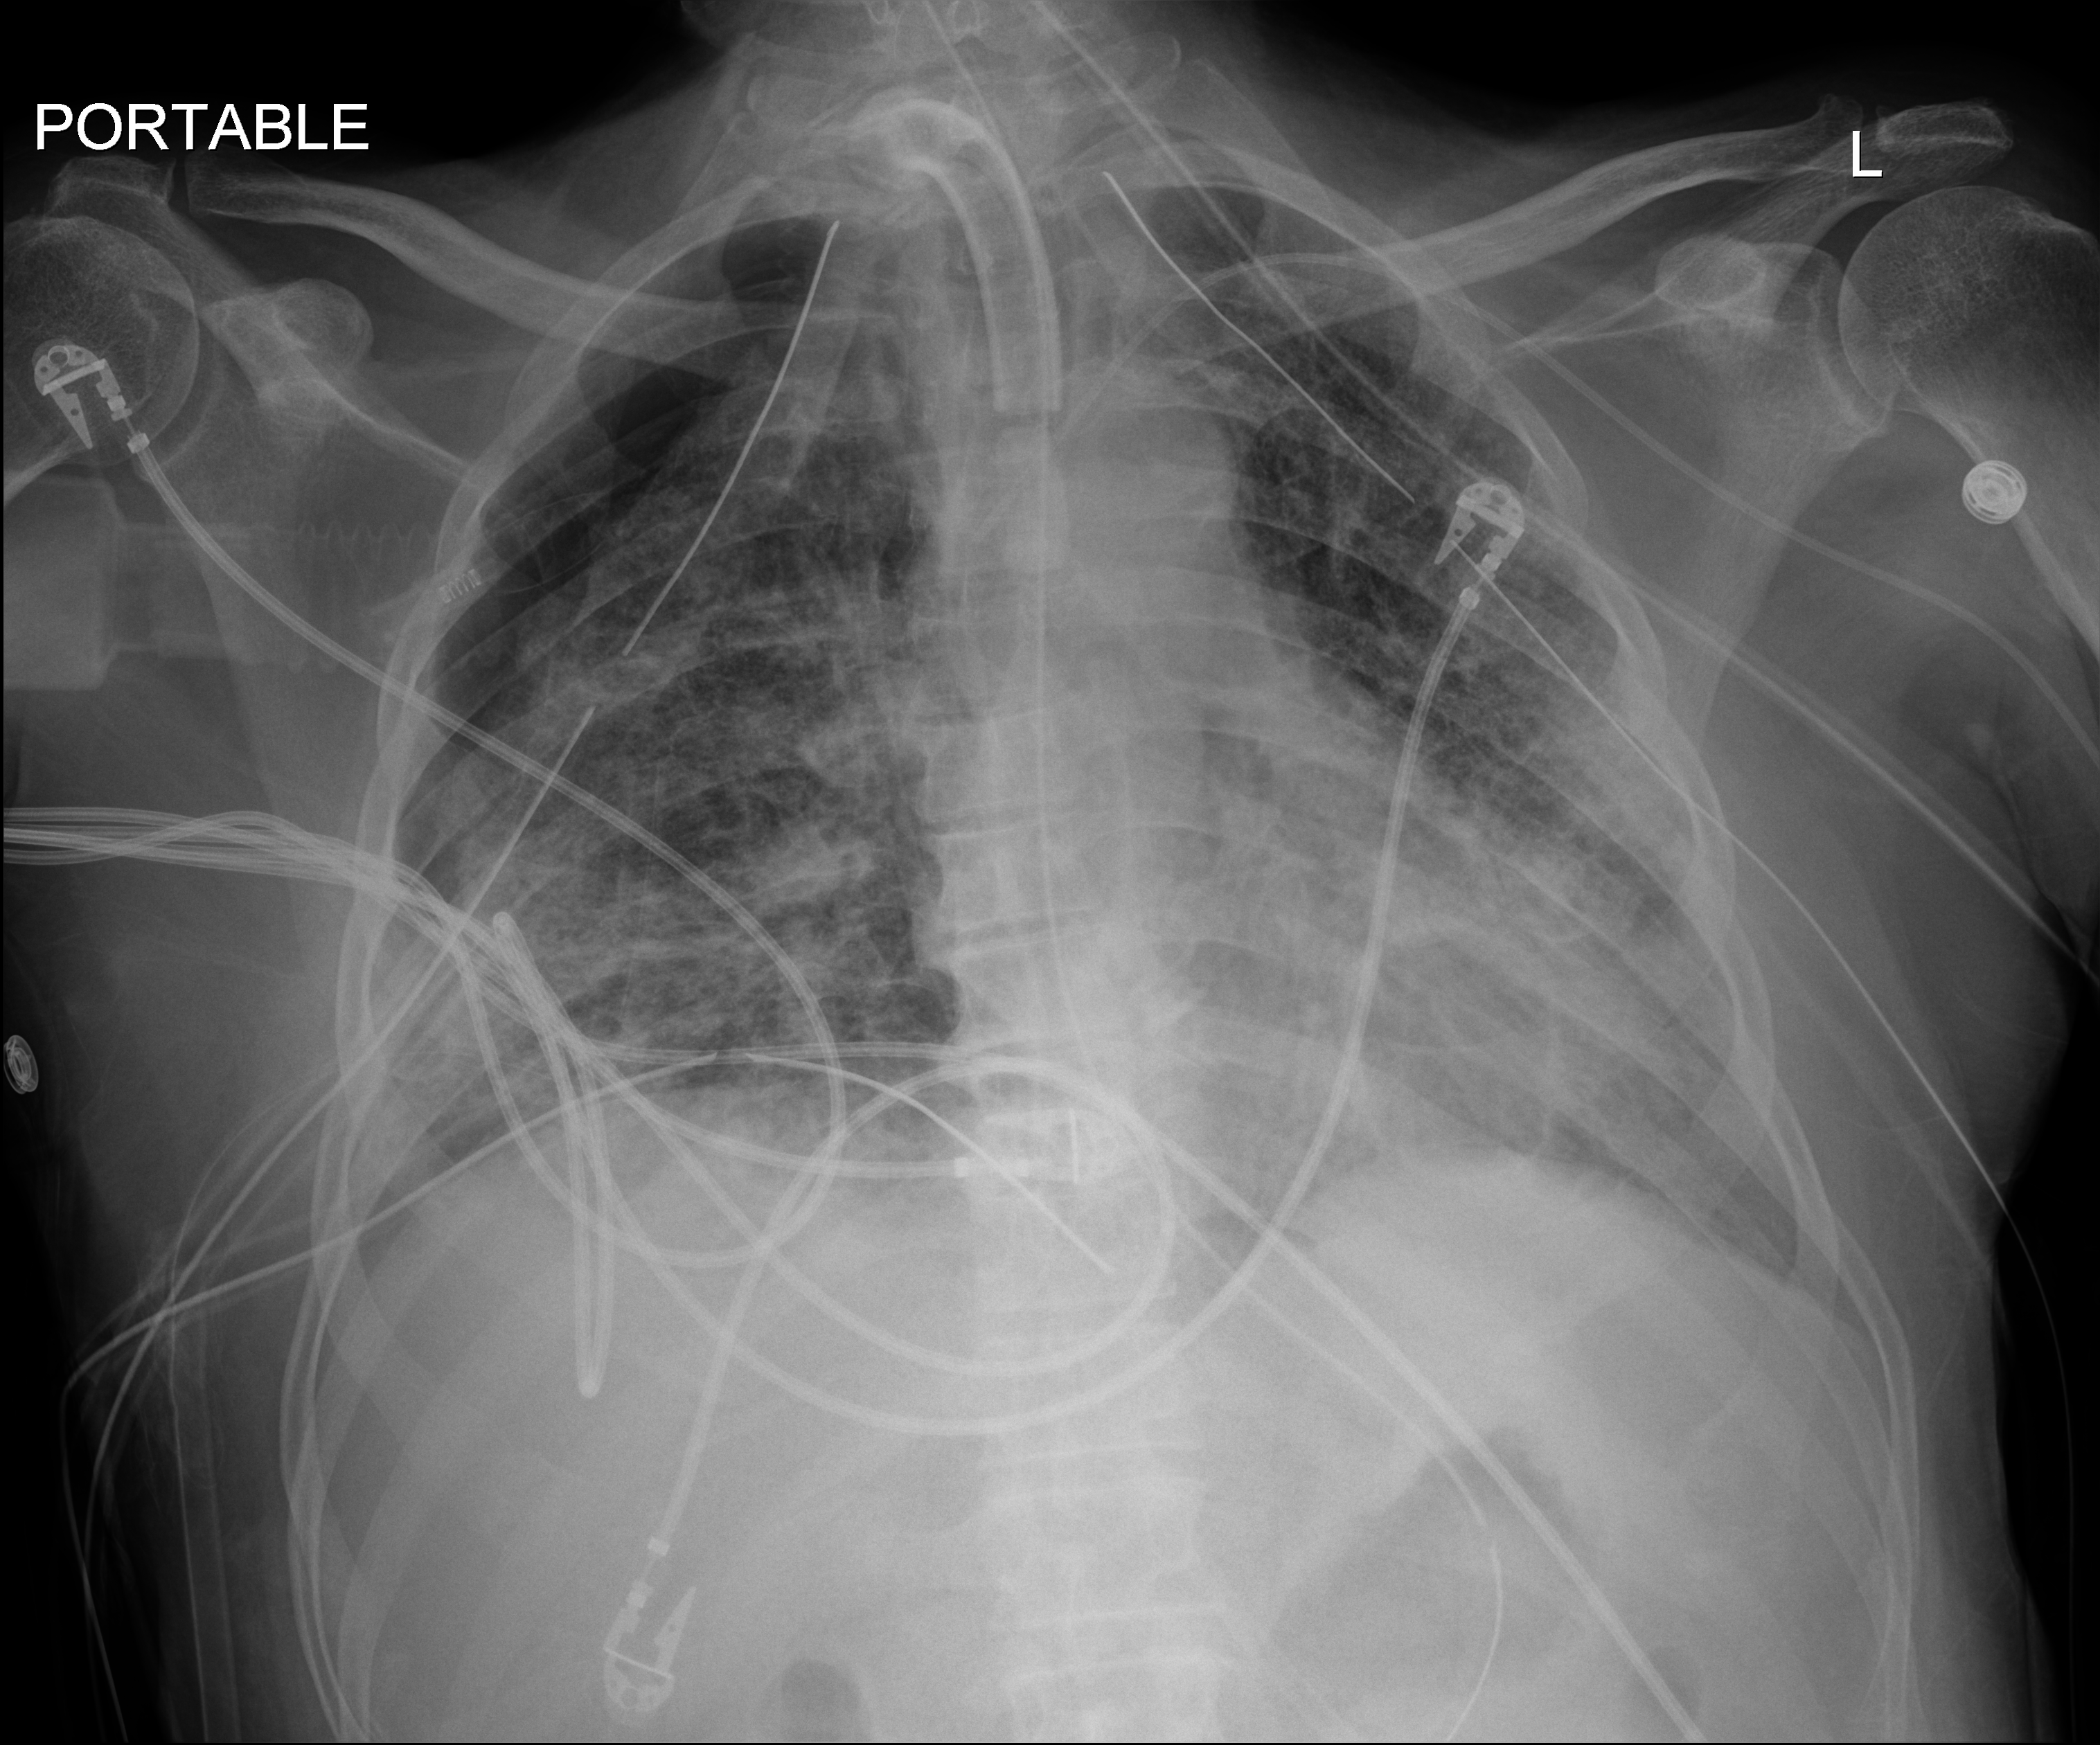
Chest X-ray (portable); anteroposterior (AP) projection. Patient hospitalised with COVID-19; male, aged 18–59 years.
Hospital-stay facts (about this admission, not read from this image; timing relative to this image not recorded):
- chronic kidney disease (admission record): no
- mechanically ventilated during this hospital stay: yes